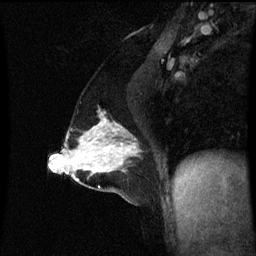
Breast MRI (dynamic contrast-enhanced), one sagittal slice. Slice 35 of 60 in the series (ordered by position). Dynamic contrast-enhanced series, image 2 of 3 at this slice position (ordered by acquisition). 1.5 T. TE 4.2 ms, TR 8.9 ms. 2.1 mm slice thickness. 256 × 256 image matrix, field of view 200 × 200 mm. Patient: female, 47 years. From the clinical record (not read from this slice): setting: breast cancer imaged before/during neoadjuvant chemotherapy; receptor status: HR-positive, HER2-negative.
Structures marked on this image (semi-automatic segmentation, software-assisted and operator-edited):
- analysis volume of interest (the breast-tissue region the enhancement analysis was run in; not a lesion): bounding box (x1, y1, x2, y2) in pixels: (71, 116, 142, 163)
- tumour enhancement mask (voxels above the 70 % enhancement threshold inside the analysis volume of interest): (94, 118, 133, 151)